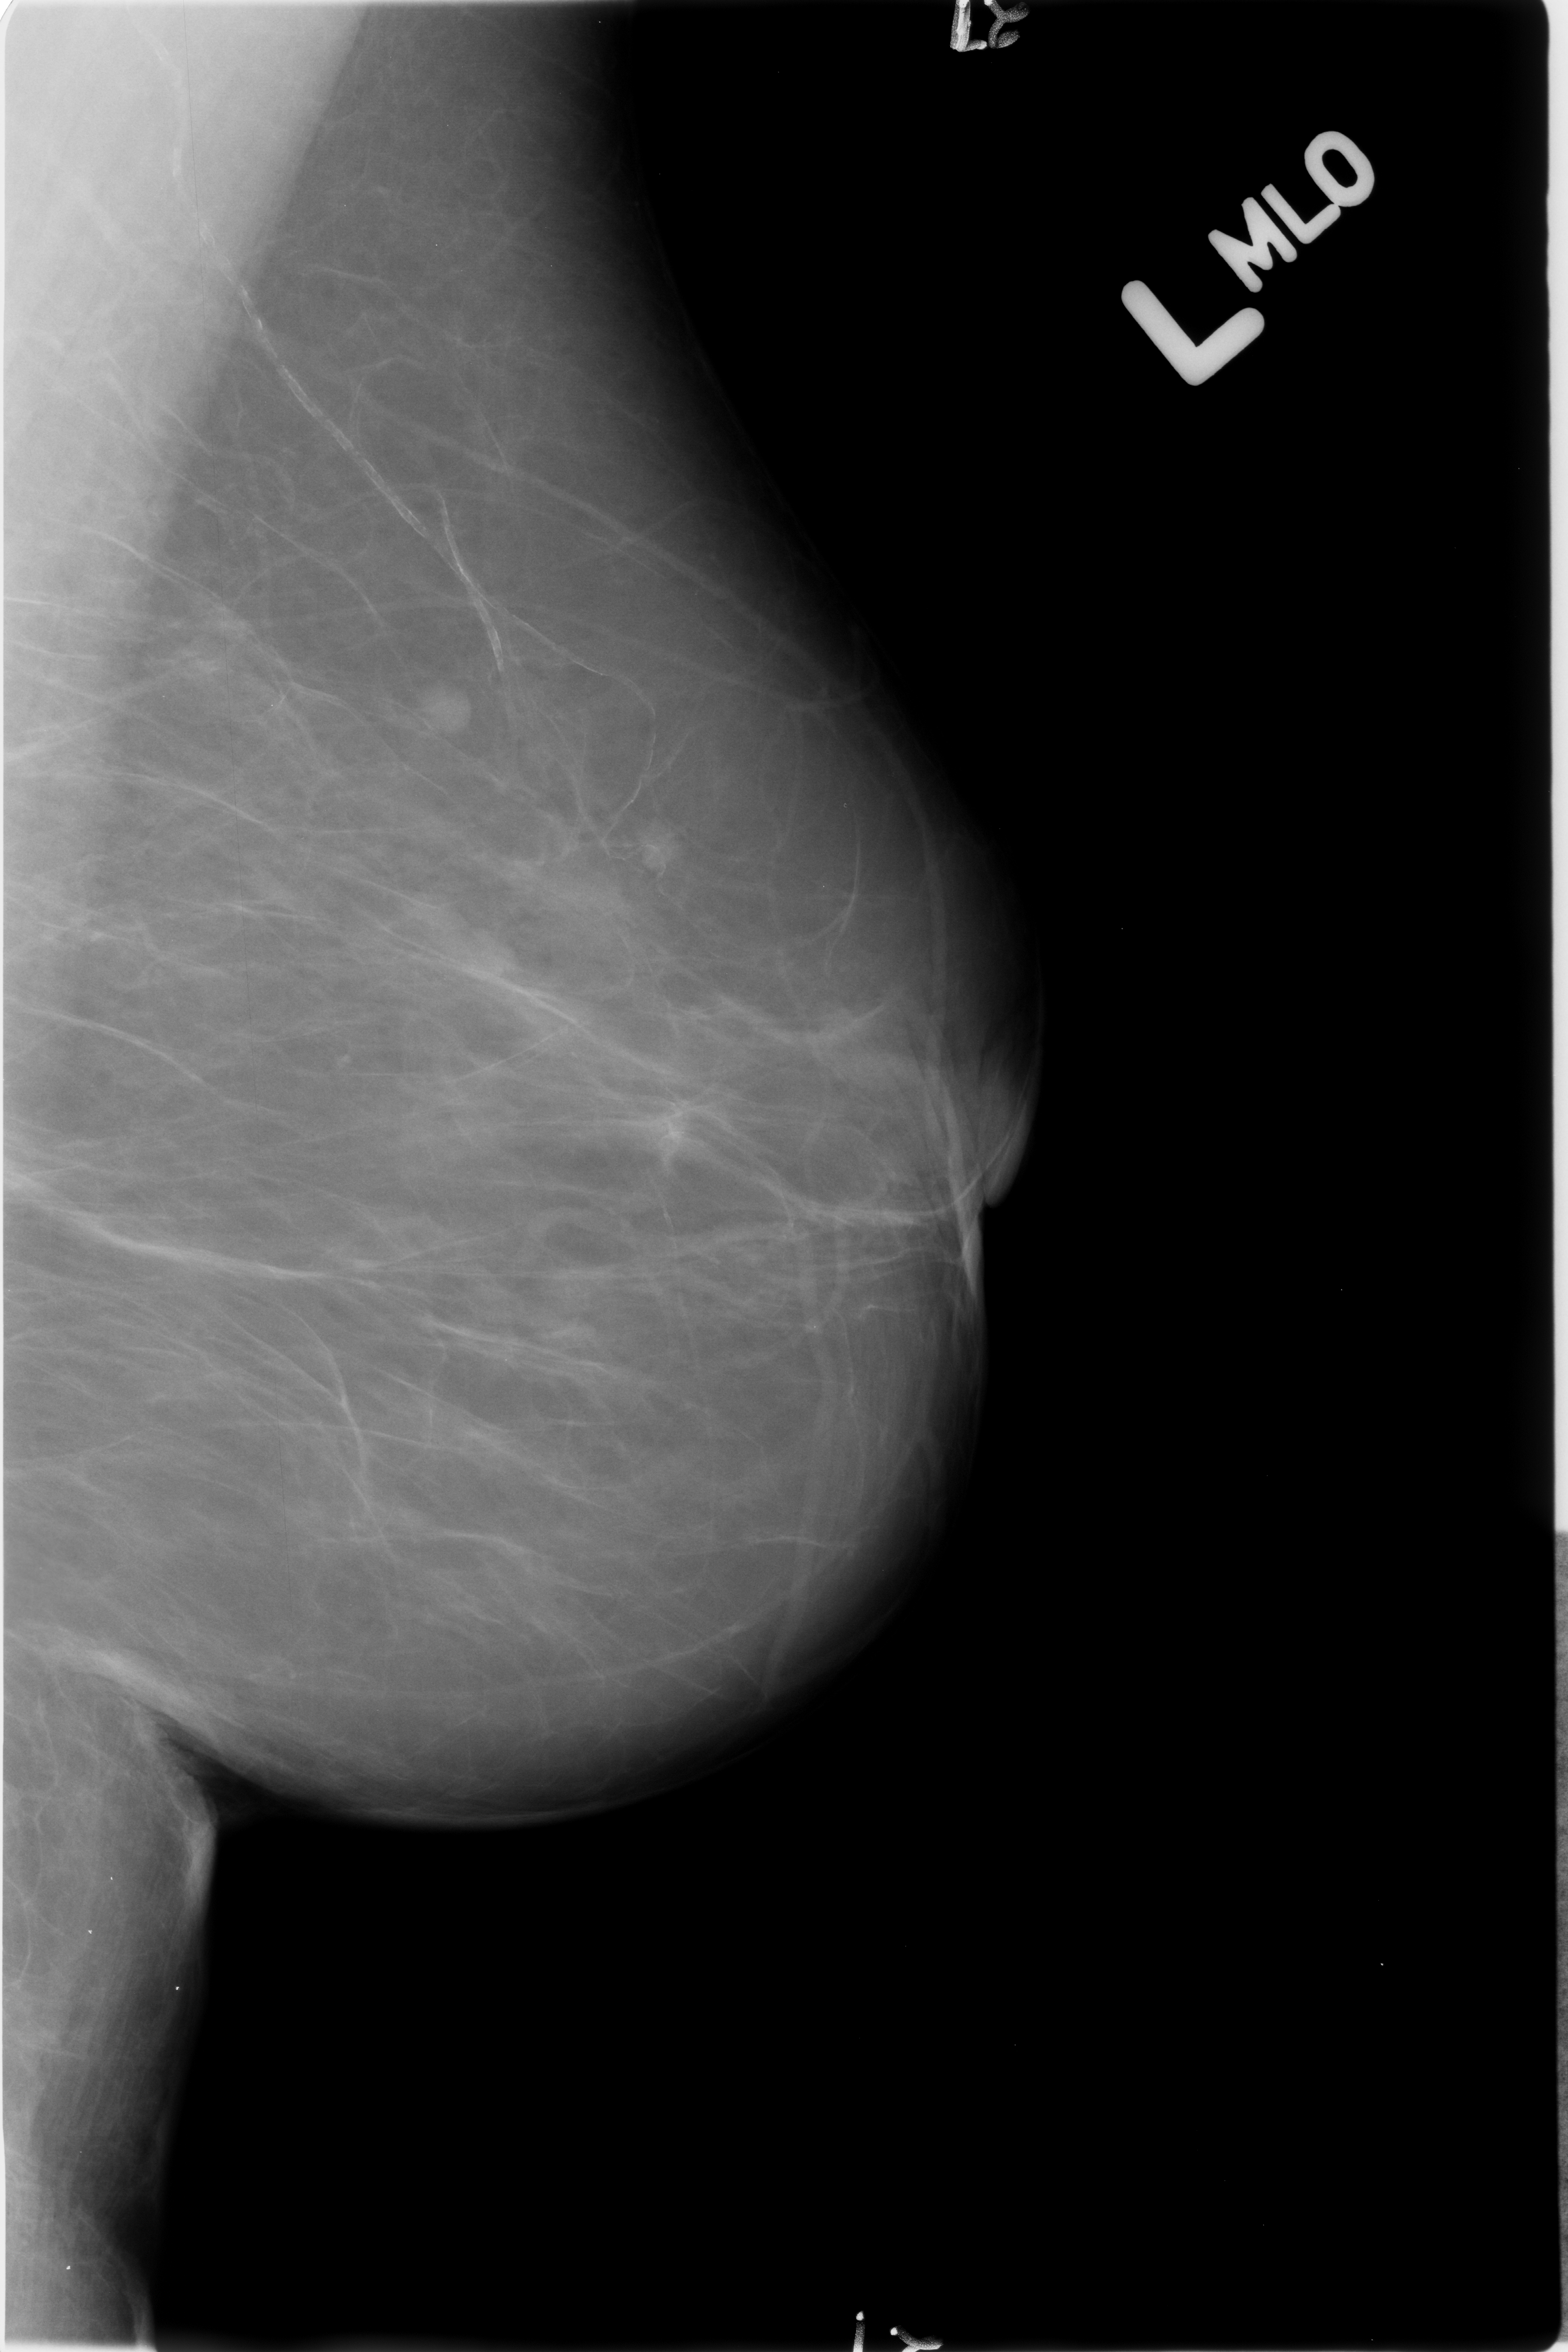
Scanned film-screen mammogram; left breast; mediolateral oblique (MLO) view; breast composition: almost entirely fatty (BI-RADS density category 1 of 4); 1568 × 2352 image matrix.
Expert-marked regions of interest on this film, with their recorded descriptors:
- calcifications, morphology vascular; BI-RADS assessment category 2; outcome (as recorded, no biopsy): benign without callback (not worked up further): bounding box [x1, y1, x2, y2] px = [136, 37, 649, 702]